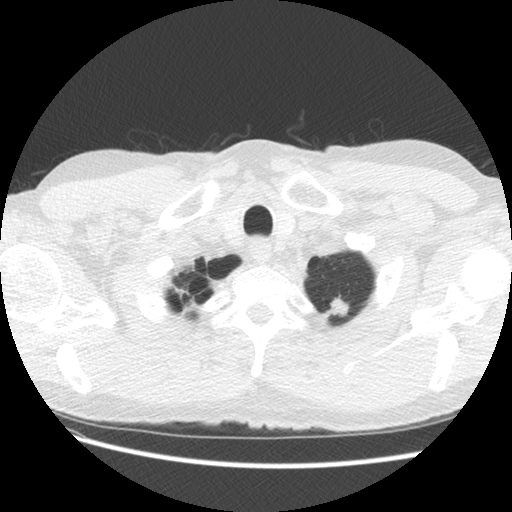
Low-dose screening chest CT, one axial slice. Slice 119 of 131 in the series (ordered by position). 140 kVp. Lung window (W 1500 / L -600 HU). 2.5 mm slice thickness. 512 × 512 image matrix.
Structures marked on this image (expert manual segmentation):
- lesion 1 (tumor, upper lobe of left lung): bounding box [x1, y1, x2, y2] px = [324, 295, 349, 320]